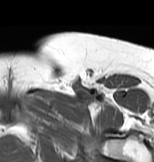
MRI of an extremity soft-tissue mass, one axial slice. Position 56 of 83 along the scan axis. MR volume resampled by the dataset authors to the PET/CT grid (not the native acquisition matrix). 3.27 mm slice thickness. 154 × 162 image matrix. Female patient. Case-level facts recorded for this patient, not image findings: histological type: myxofibrosarcoma; grade: intermediate; site of the primary tumour: left thigh.
Structures marked on this image (expert contour drawn on MRI and transferred to this co-registered scan by the dataset authors):
- gross tumour volume including surrounding oedema: bounding box (x1, y1, x2, y2) in pixels: (39, 89, 114, 115)